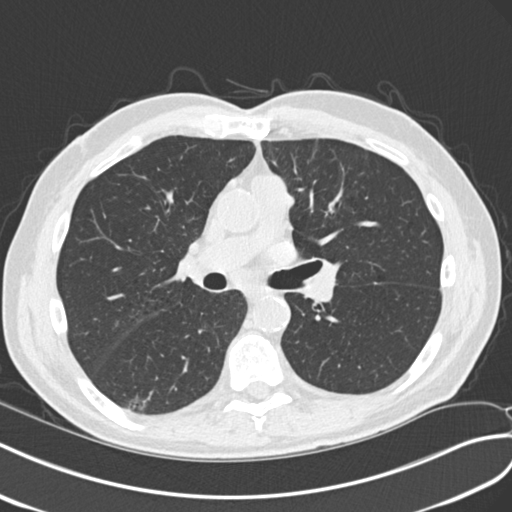
Low-dose screening chest CT, axial slice; second annual screen; lung window (W 1500 / L -600 HU); 2 mm slice thickness; standard (soft-tissue) reconstruction kernel (B30f); 120 kVp. Male participant, aged 68 years at enrolment.
Expert reader's lesion annotation, bounding box [x1, y1, x2, y2] px = [113, 386, 162, 422]. The screening reader recorded 4 non-calcified nodules or masses ≥4 mm on this exam; which of them this box marks is not recorded. Lung cancer was diagnosed 653 days after this screen: non-small cell carcinoma, right lower lobe, poorly differentiated (G3), stage IA (AJCC 6th edition), 23 mm at pathology.